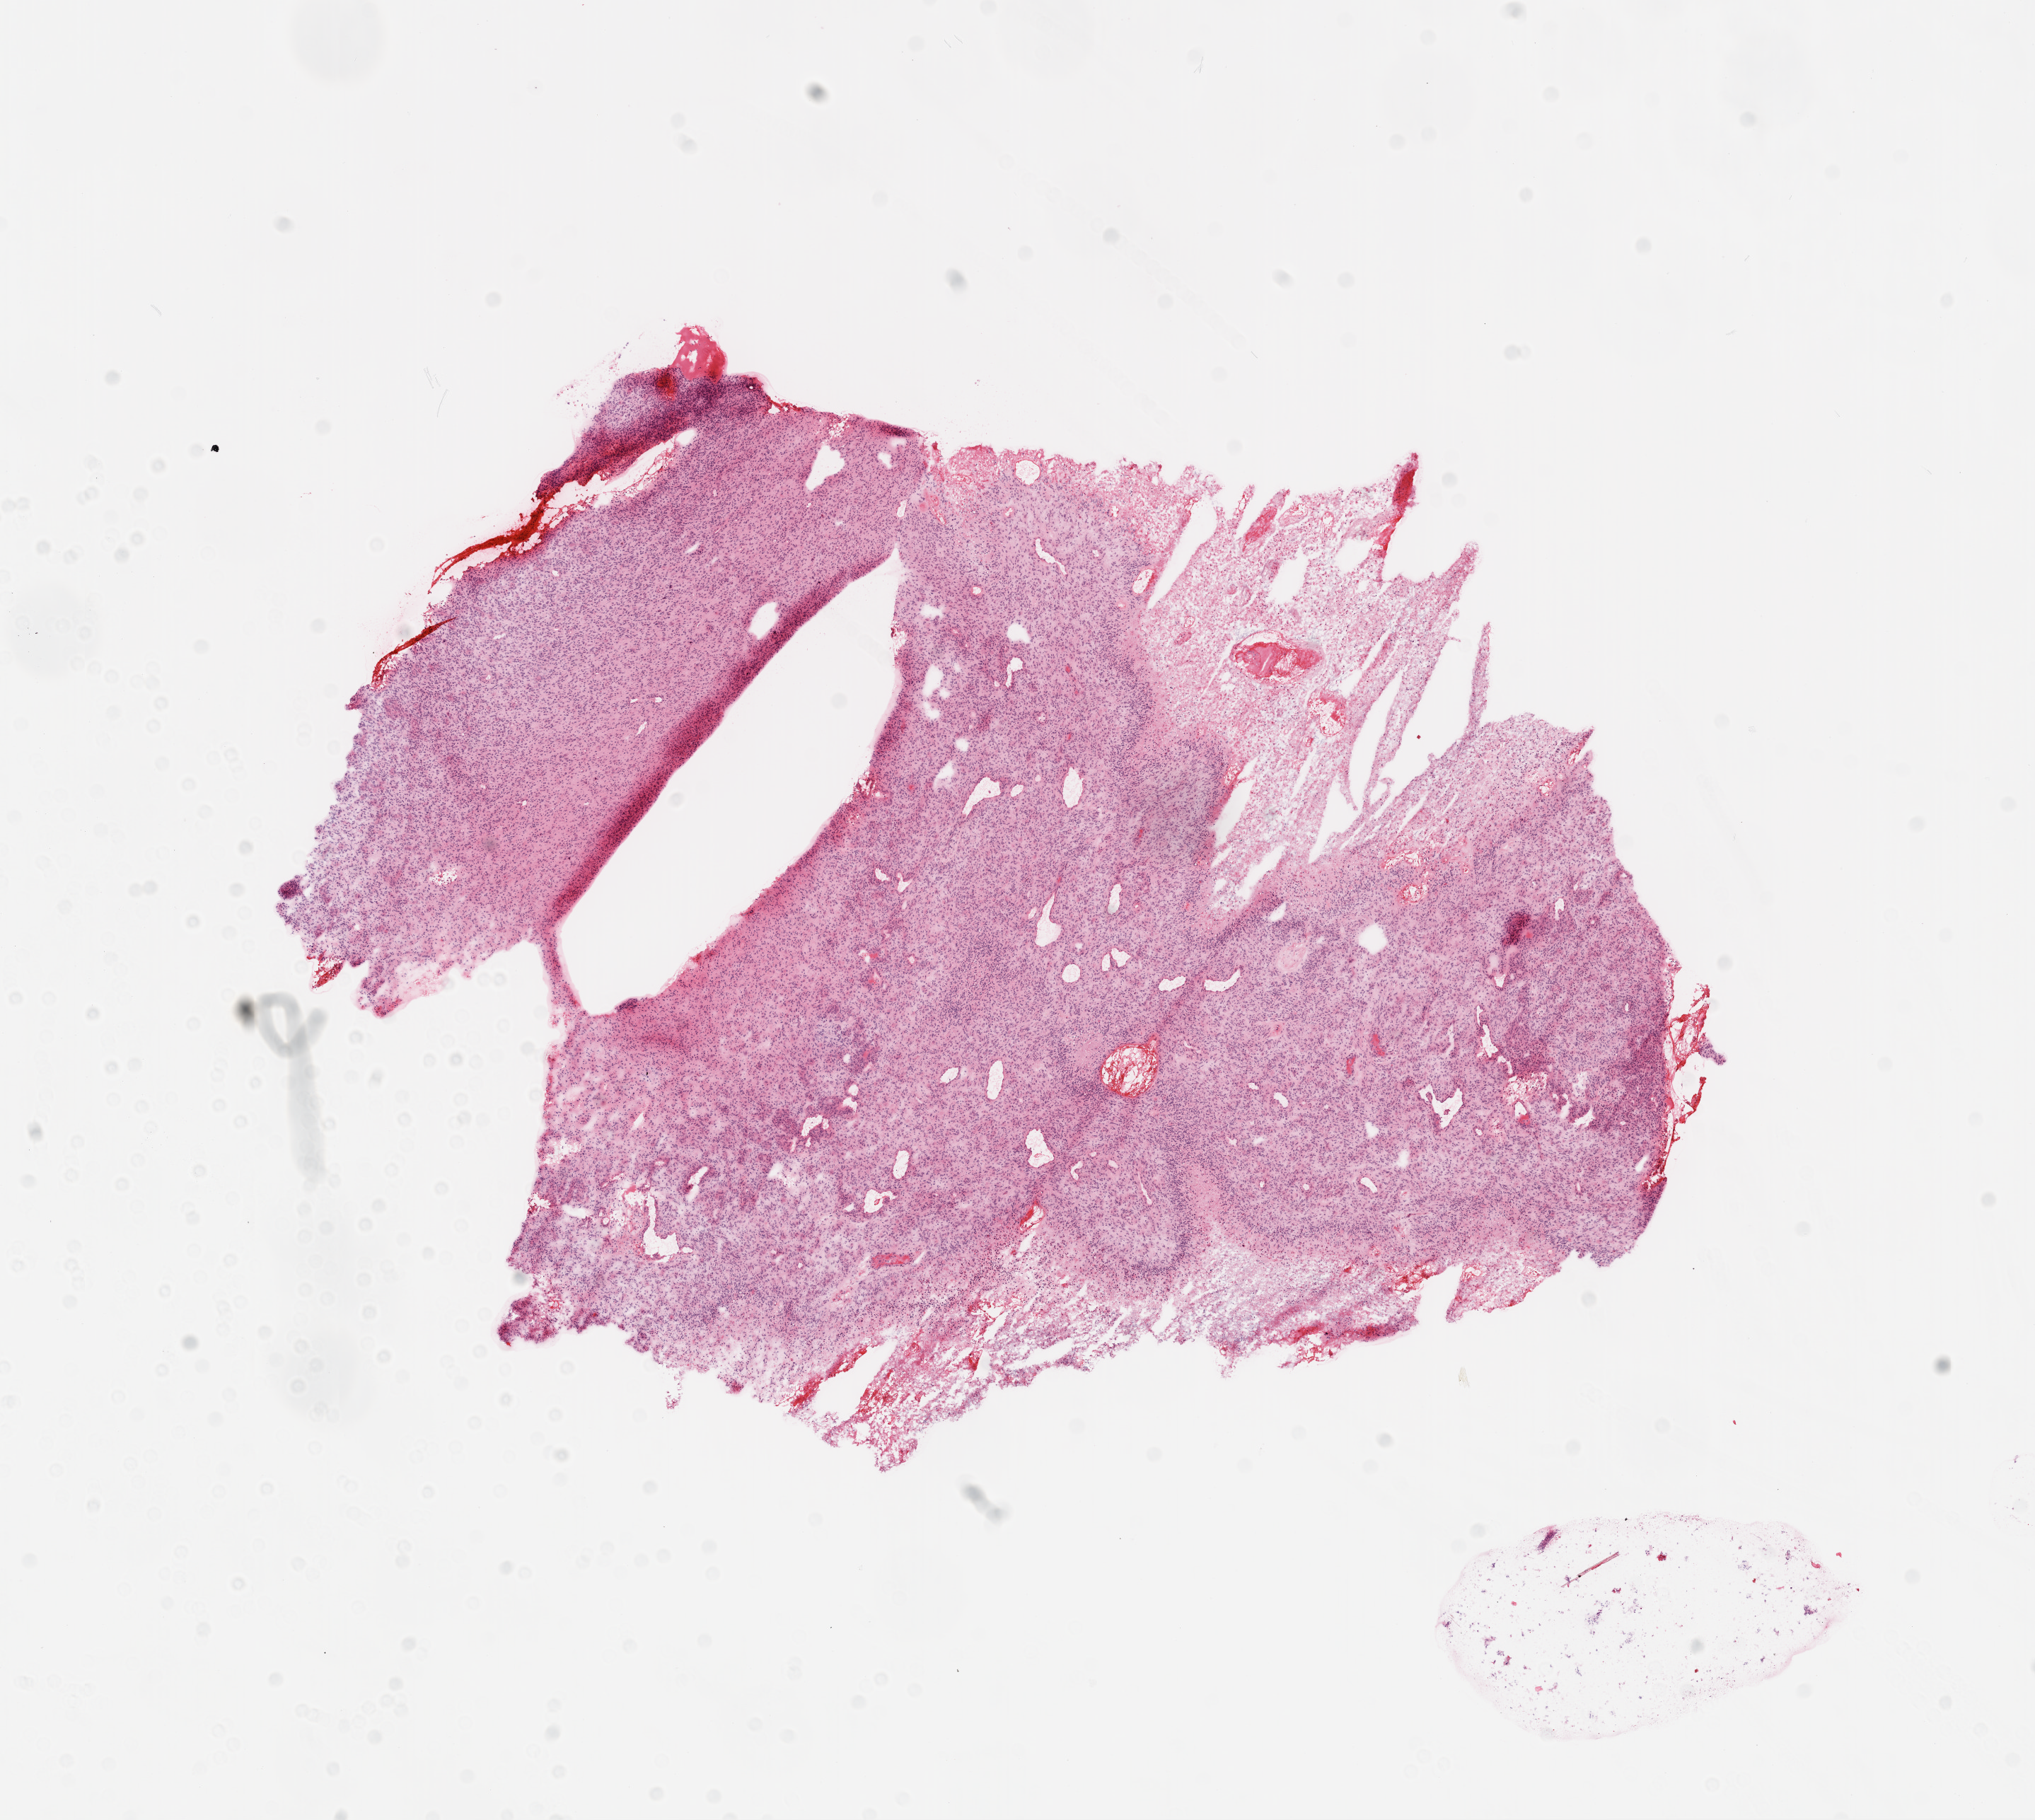
Digitized H&E tissue section (whole slide), shown as a low-resolution overview of the whole scanned area (about 11.6 x 10.4 mm, acquisition: 20x scan), frozen section, sample: primary tumour, brain. Patient: male, age at initial diagnosis 49 years. Composition of this section per pathologist review: tumour cells 90%, tumour nuclei 95%, normal cells 0%, stromal cells 0%, necrosis 10%.
- pathologic diagnosis: Glioblastoma